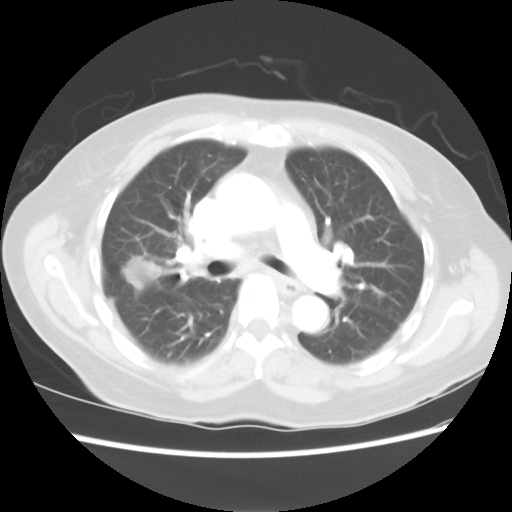
Chest CT, one axial slice. Slice 42 of 80 in the series (ordered by position). Reconstruction kernel STANDARD. 100 kVp. Lung window (W 1500 / L -600 HU). 5 mm slice thickness. 512 × 512 image matrix, field of view 342 × 342 mm. Female patient, age 67 years. Case-level facts recorded for this patient, not image findings: clinical TNM (as recorded): T1c N1 M0.
Outlined on this slice (bounding box drawn by a radiologist):
- lung tumour (recorded histology: adenocarcinoma): bounding box (x1, y1, x2, y2) in pixels: (117, 246, 169, 296)